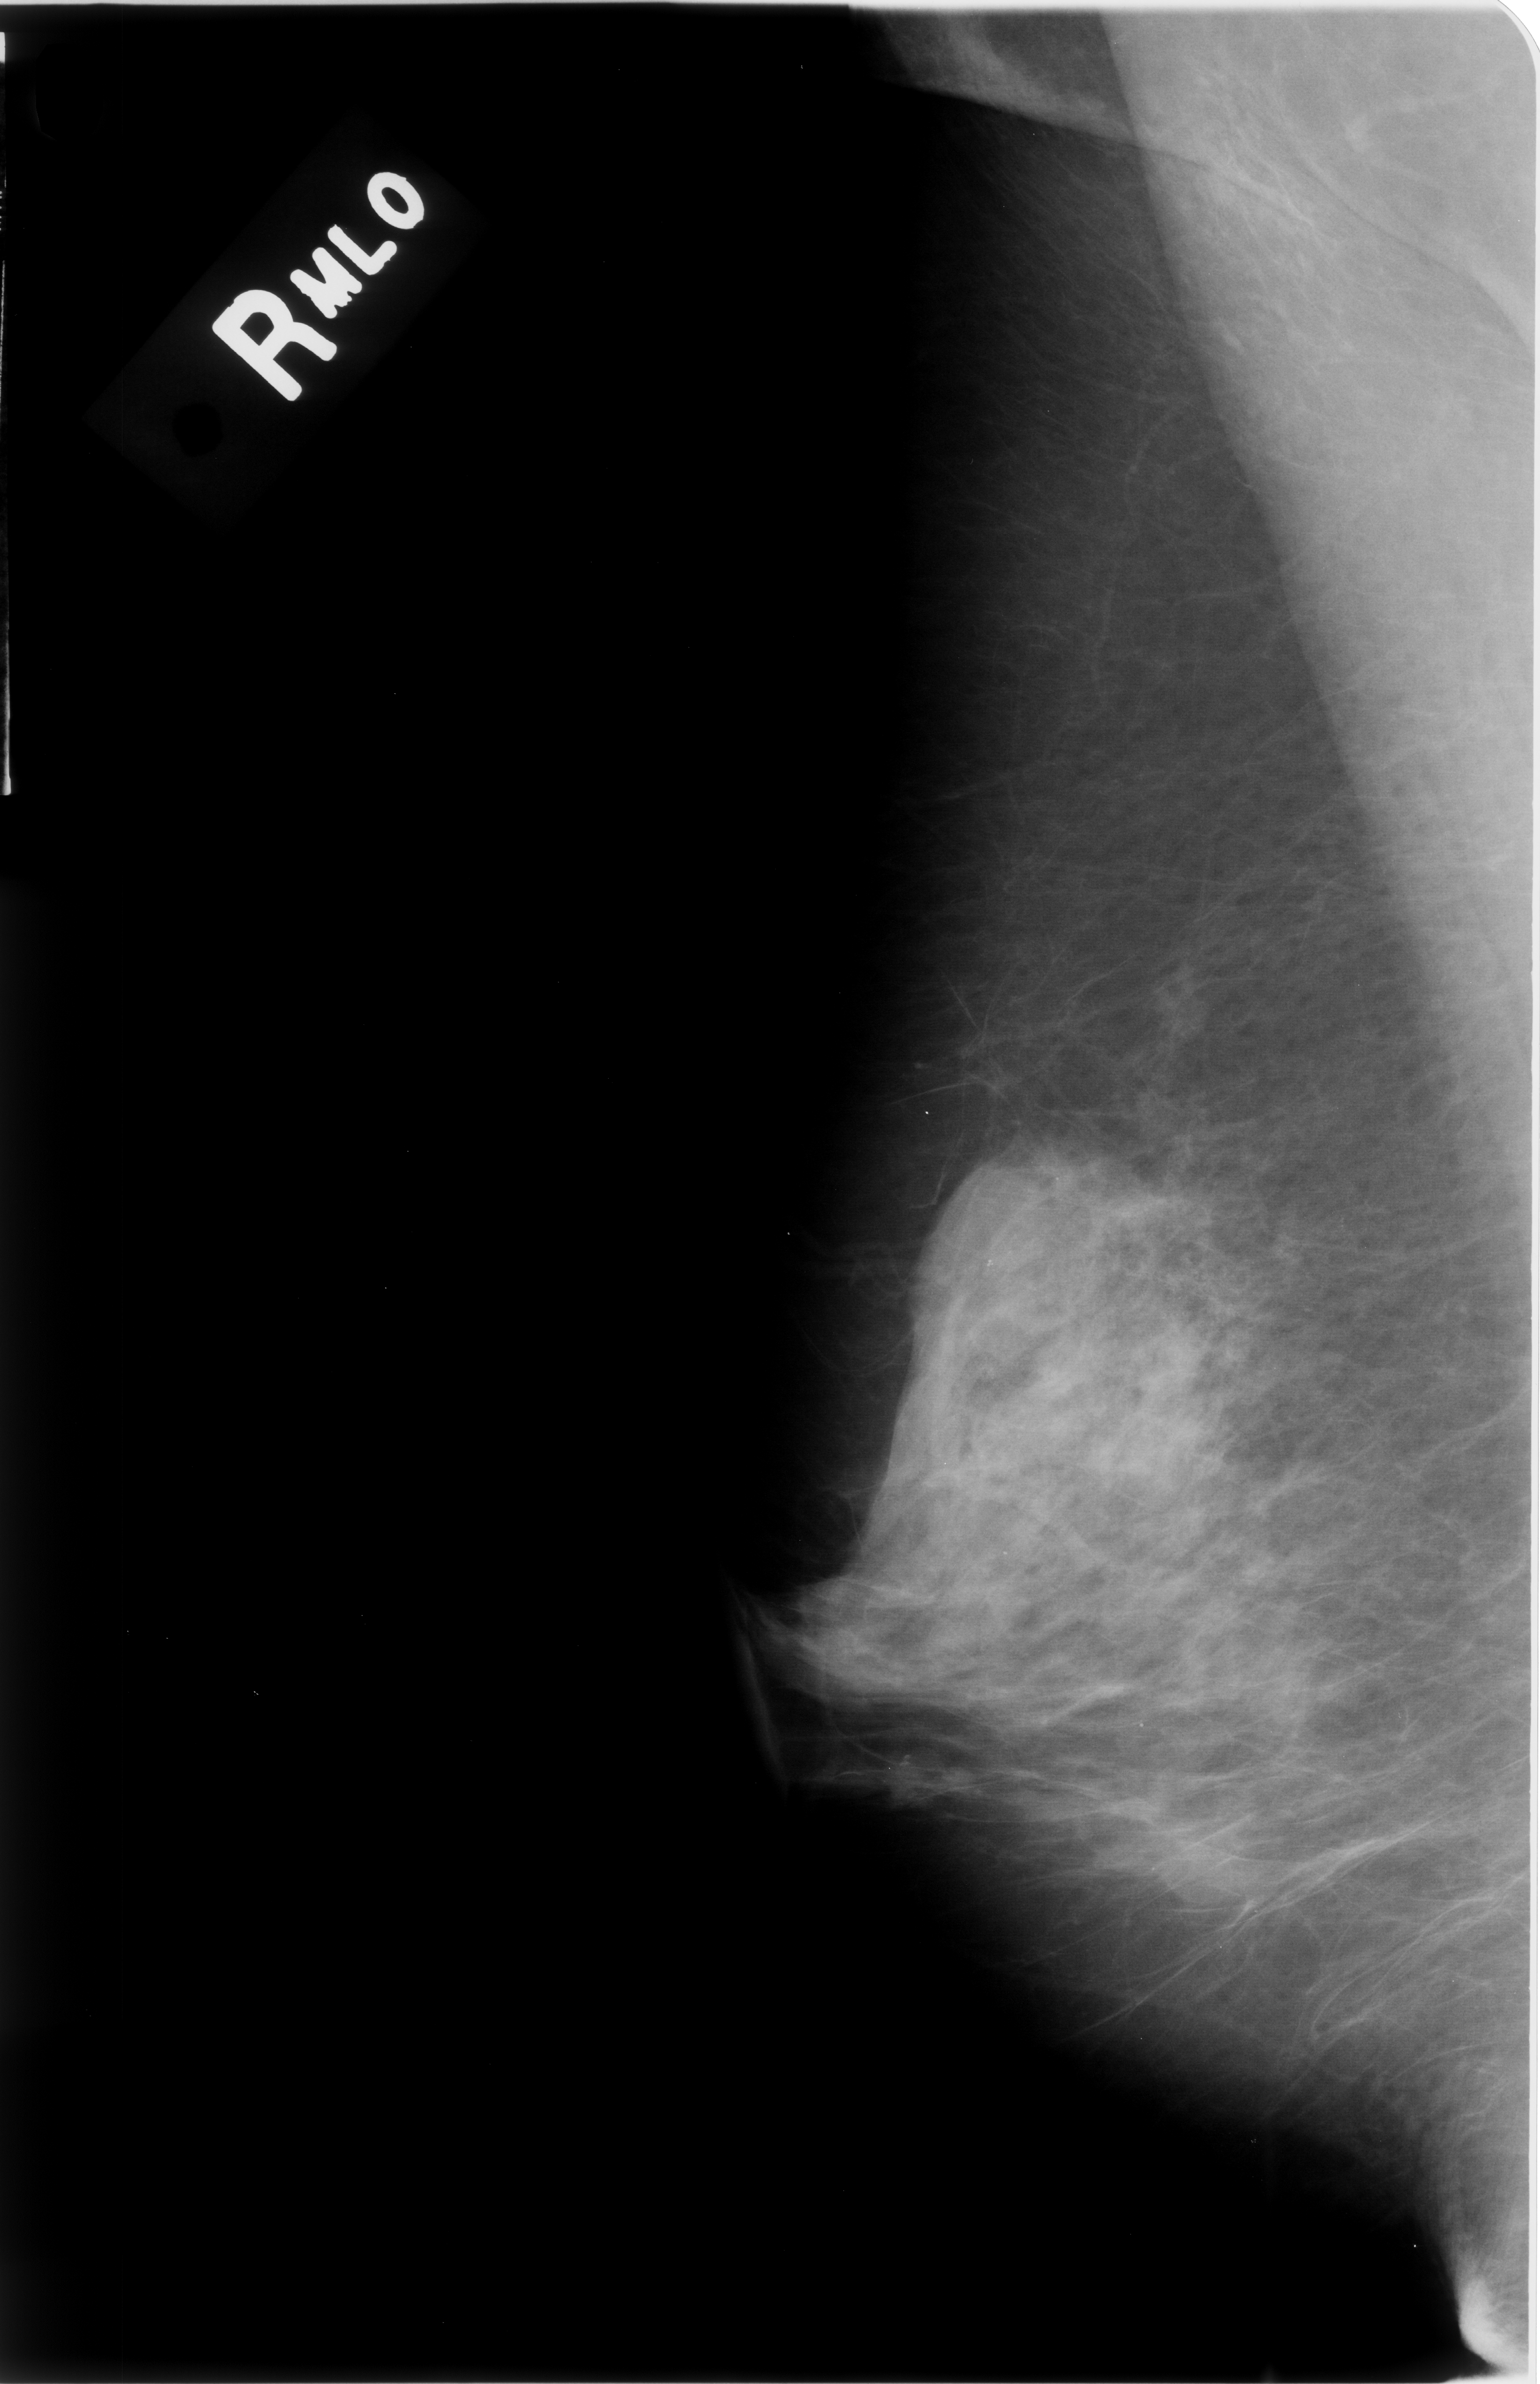
Mammogram (digitized film), right breast, mediolateral oblique (MLO) view, breast composition: heterogeneously dense (BI-RADS density category 3 of 4).
Abnormality record for this image: Finding 1 of 2: calcifications, morphology amorphous, distribution clustered; BI-RADS assessment category 4; pathology result (as recorded, not read from the image): malignant. Finding 2 of 2: calcifications, morphology amorphous, distribution clustered; BI-RADS assessment category 4; pathology result (as recorded, not read from the image): benign.